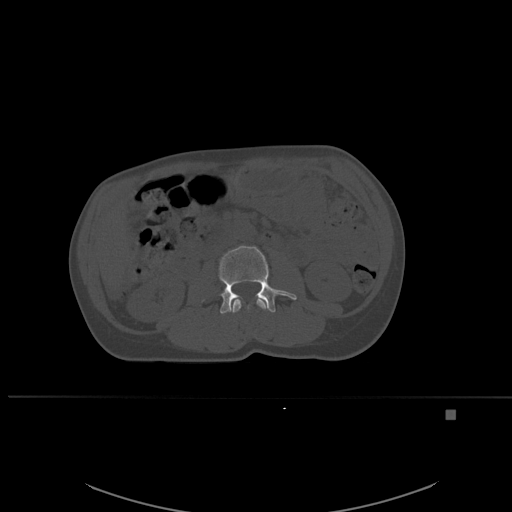
CT including the spine, one axial slice. Position 220 of 537 along the scan axis. Bone window (W 1800 / L 400 HU). 512 × 512 image matrix. Patient: female, 45 years. Case-level facts recorded for this patient, not image findings: primary cancer: lung.
Annotated regions visible in this slice (semi-automatic segmentation, software-assisted and operator-edited):
- L2 vertebra: bounding box <231,296,268,313> (left, top, right, bottom; pixels)
- L3 vertebra: <218,245,297,314>